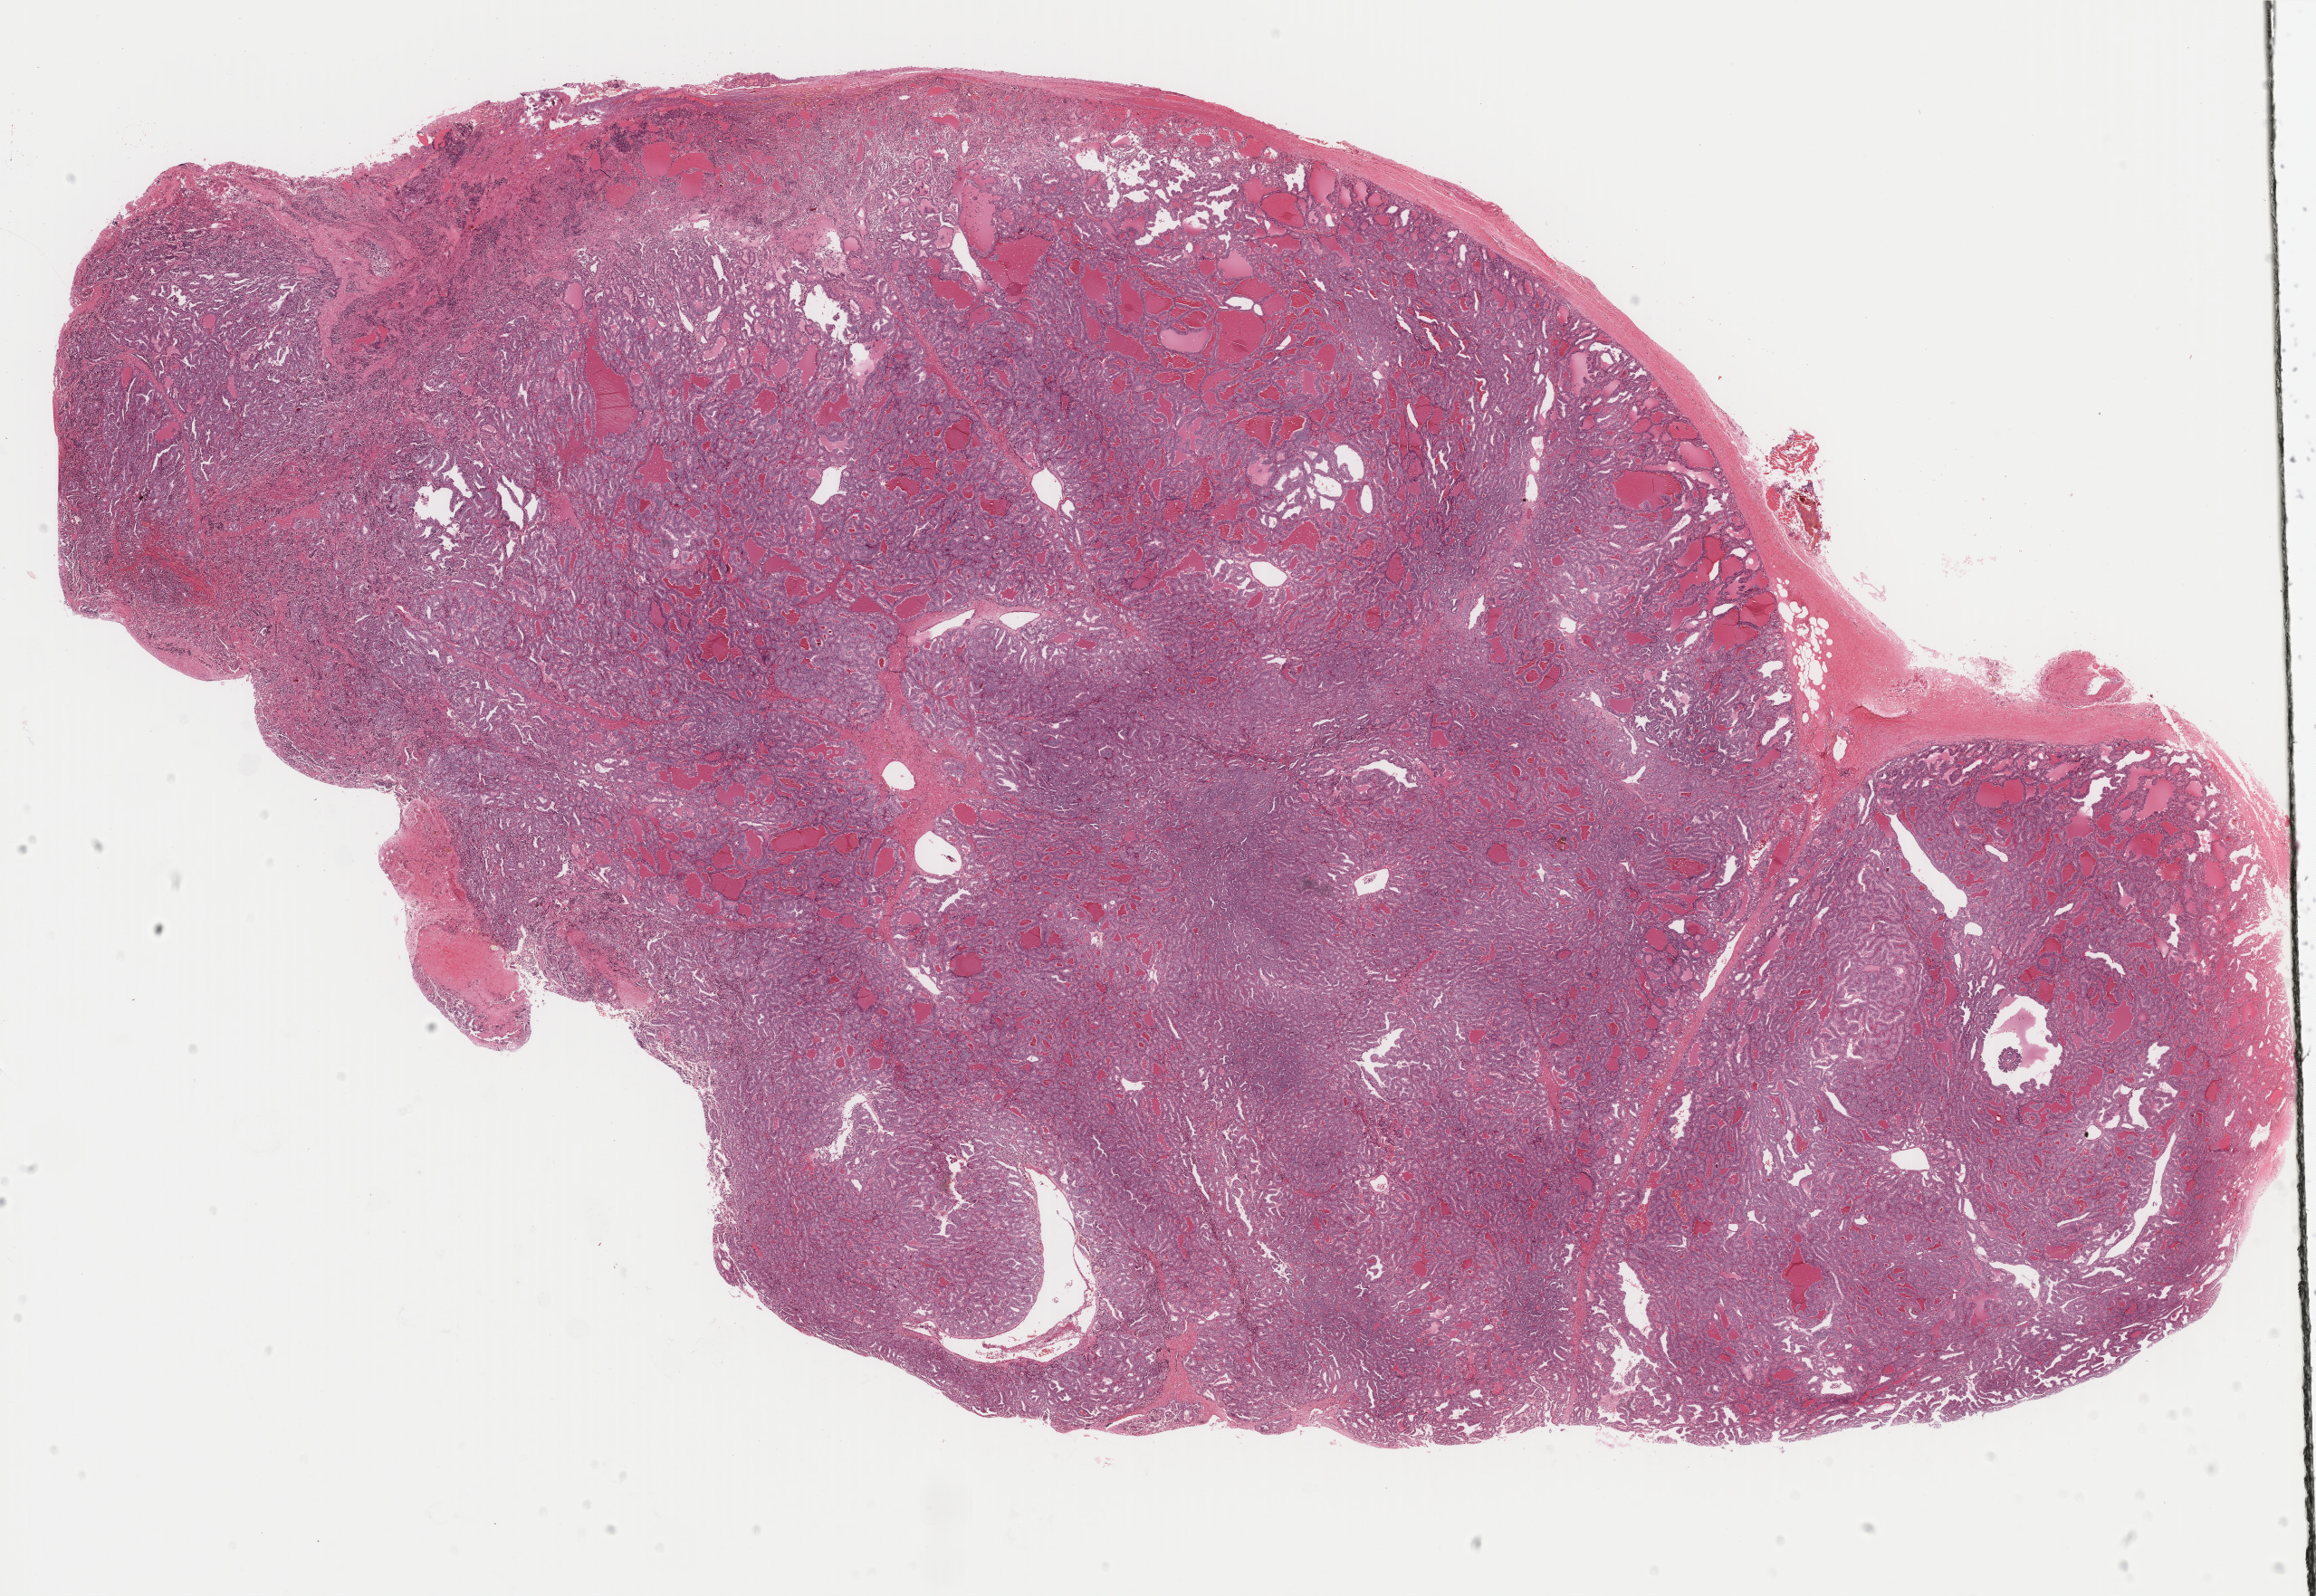
Hematoxylin and eosin (H&E) stained whole-slide image, a low-resolution overview of the entire scanned area, about 20.3 x 14.0 mm. FFPE section. Thyroid, primary tumour sample. Female, age 37 years at initial diagnosis.
Diagnosis: Papillary adenocarcinoma, NOS (thyroid gland). Lymph nodes positive (case pathology): 2 of 4 examined. AJCC pathologic stage: I (7th edition).